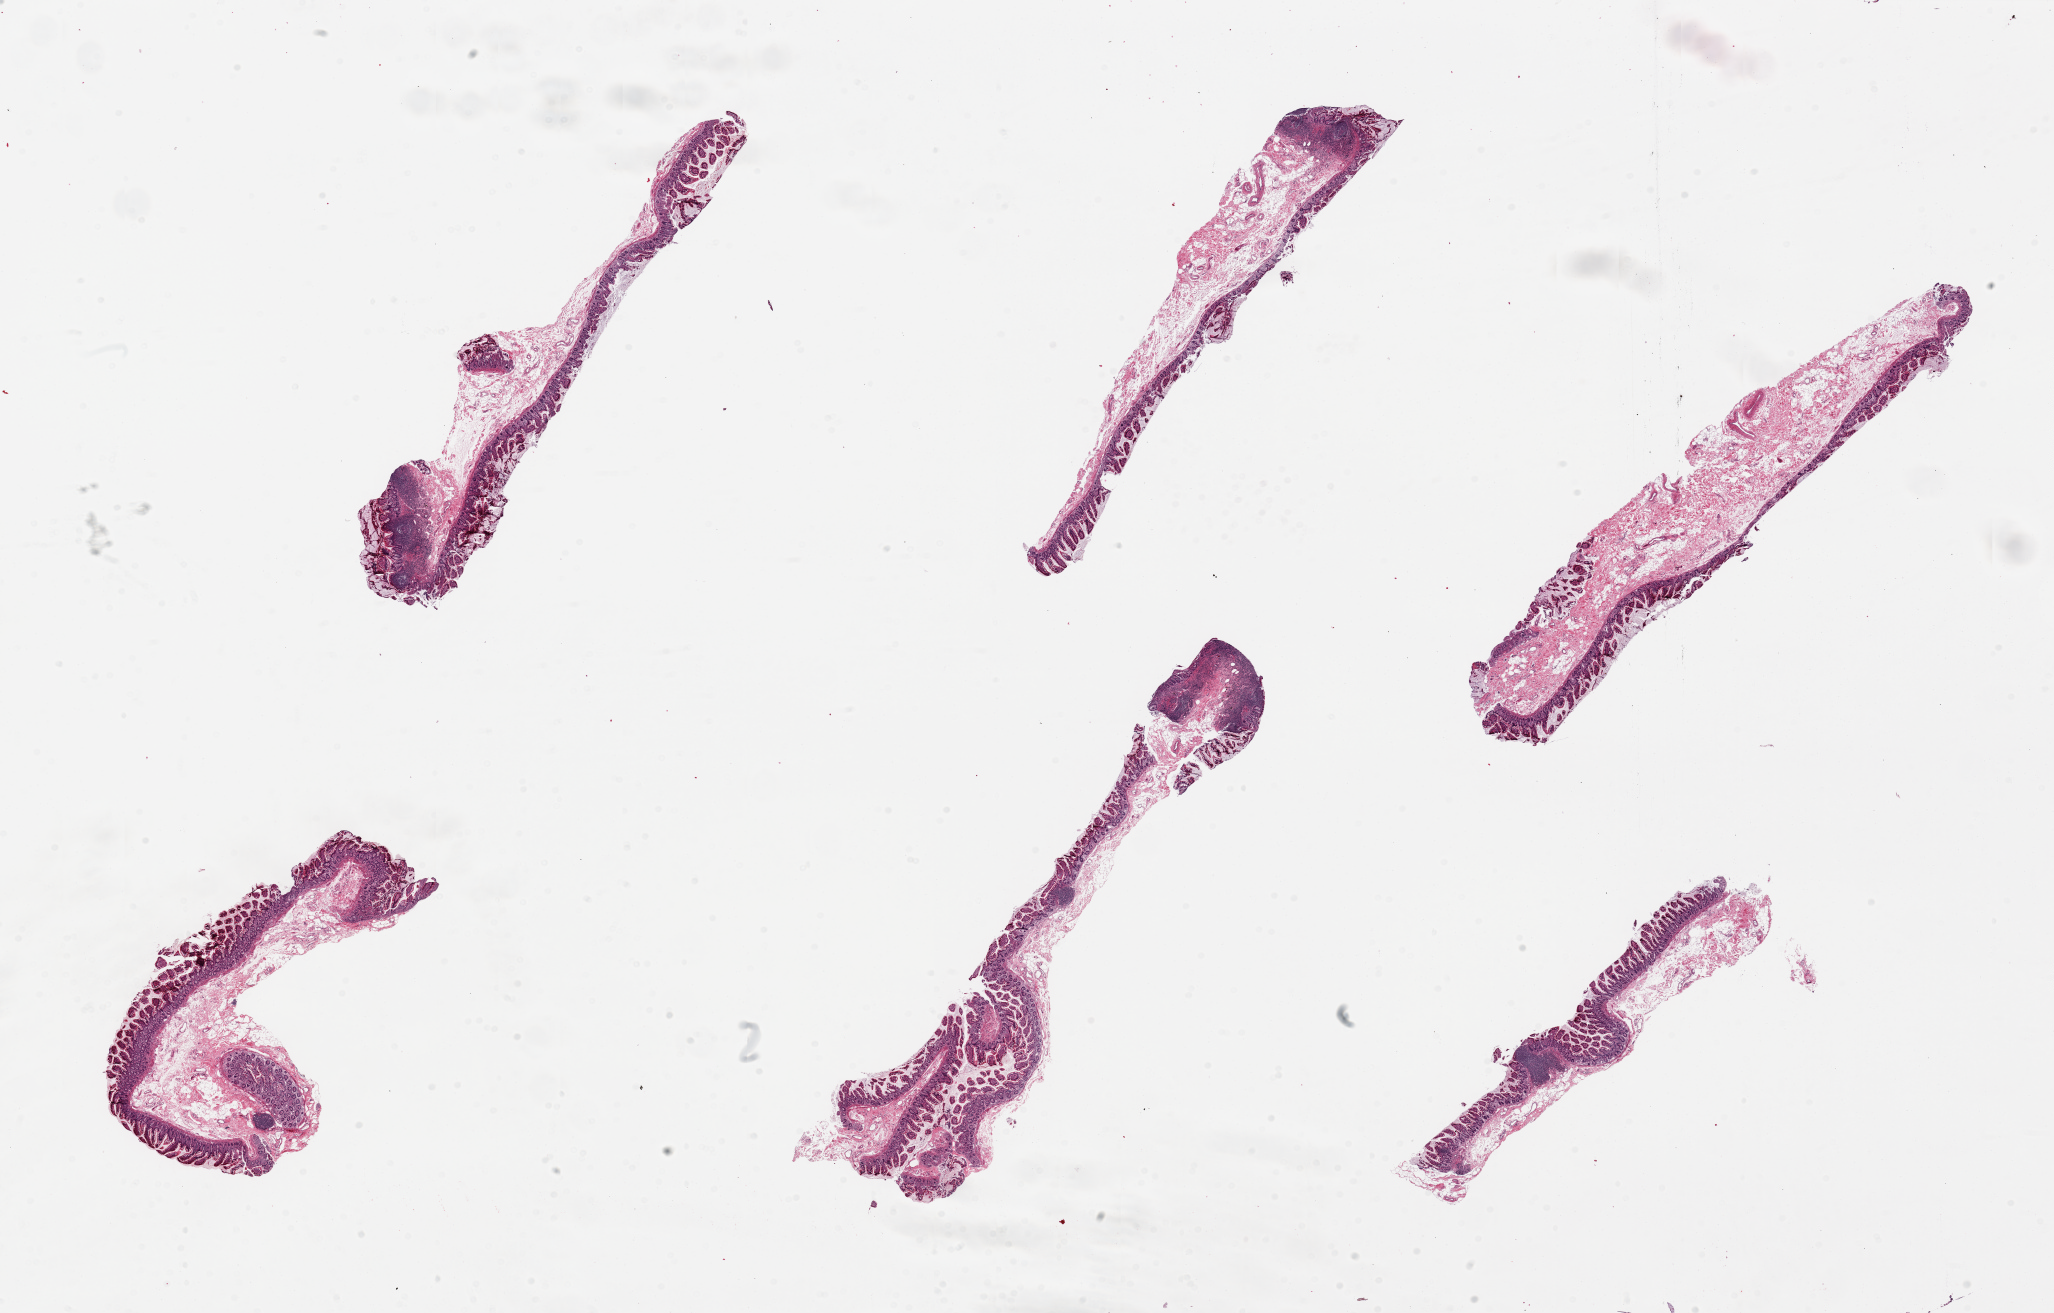
Digitized haematoxylin and eosin-stained section — whole scanned area (about 32.5 x 20.8 mm) shown as a low-resolution overview; PAXgene-fixed paraffin-embedded (PFPE) section; target tissue: ileum; tissue donor sample. Male donor.
* reviewer comment on this tissue sample: 6 pieces. up to 11x3mm; Well dissected mucosa with several lymphoid nodules marked